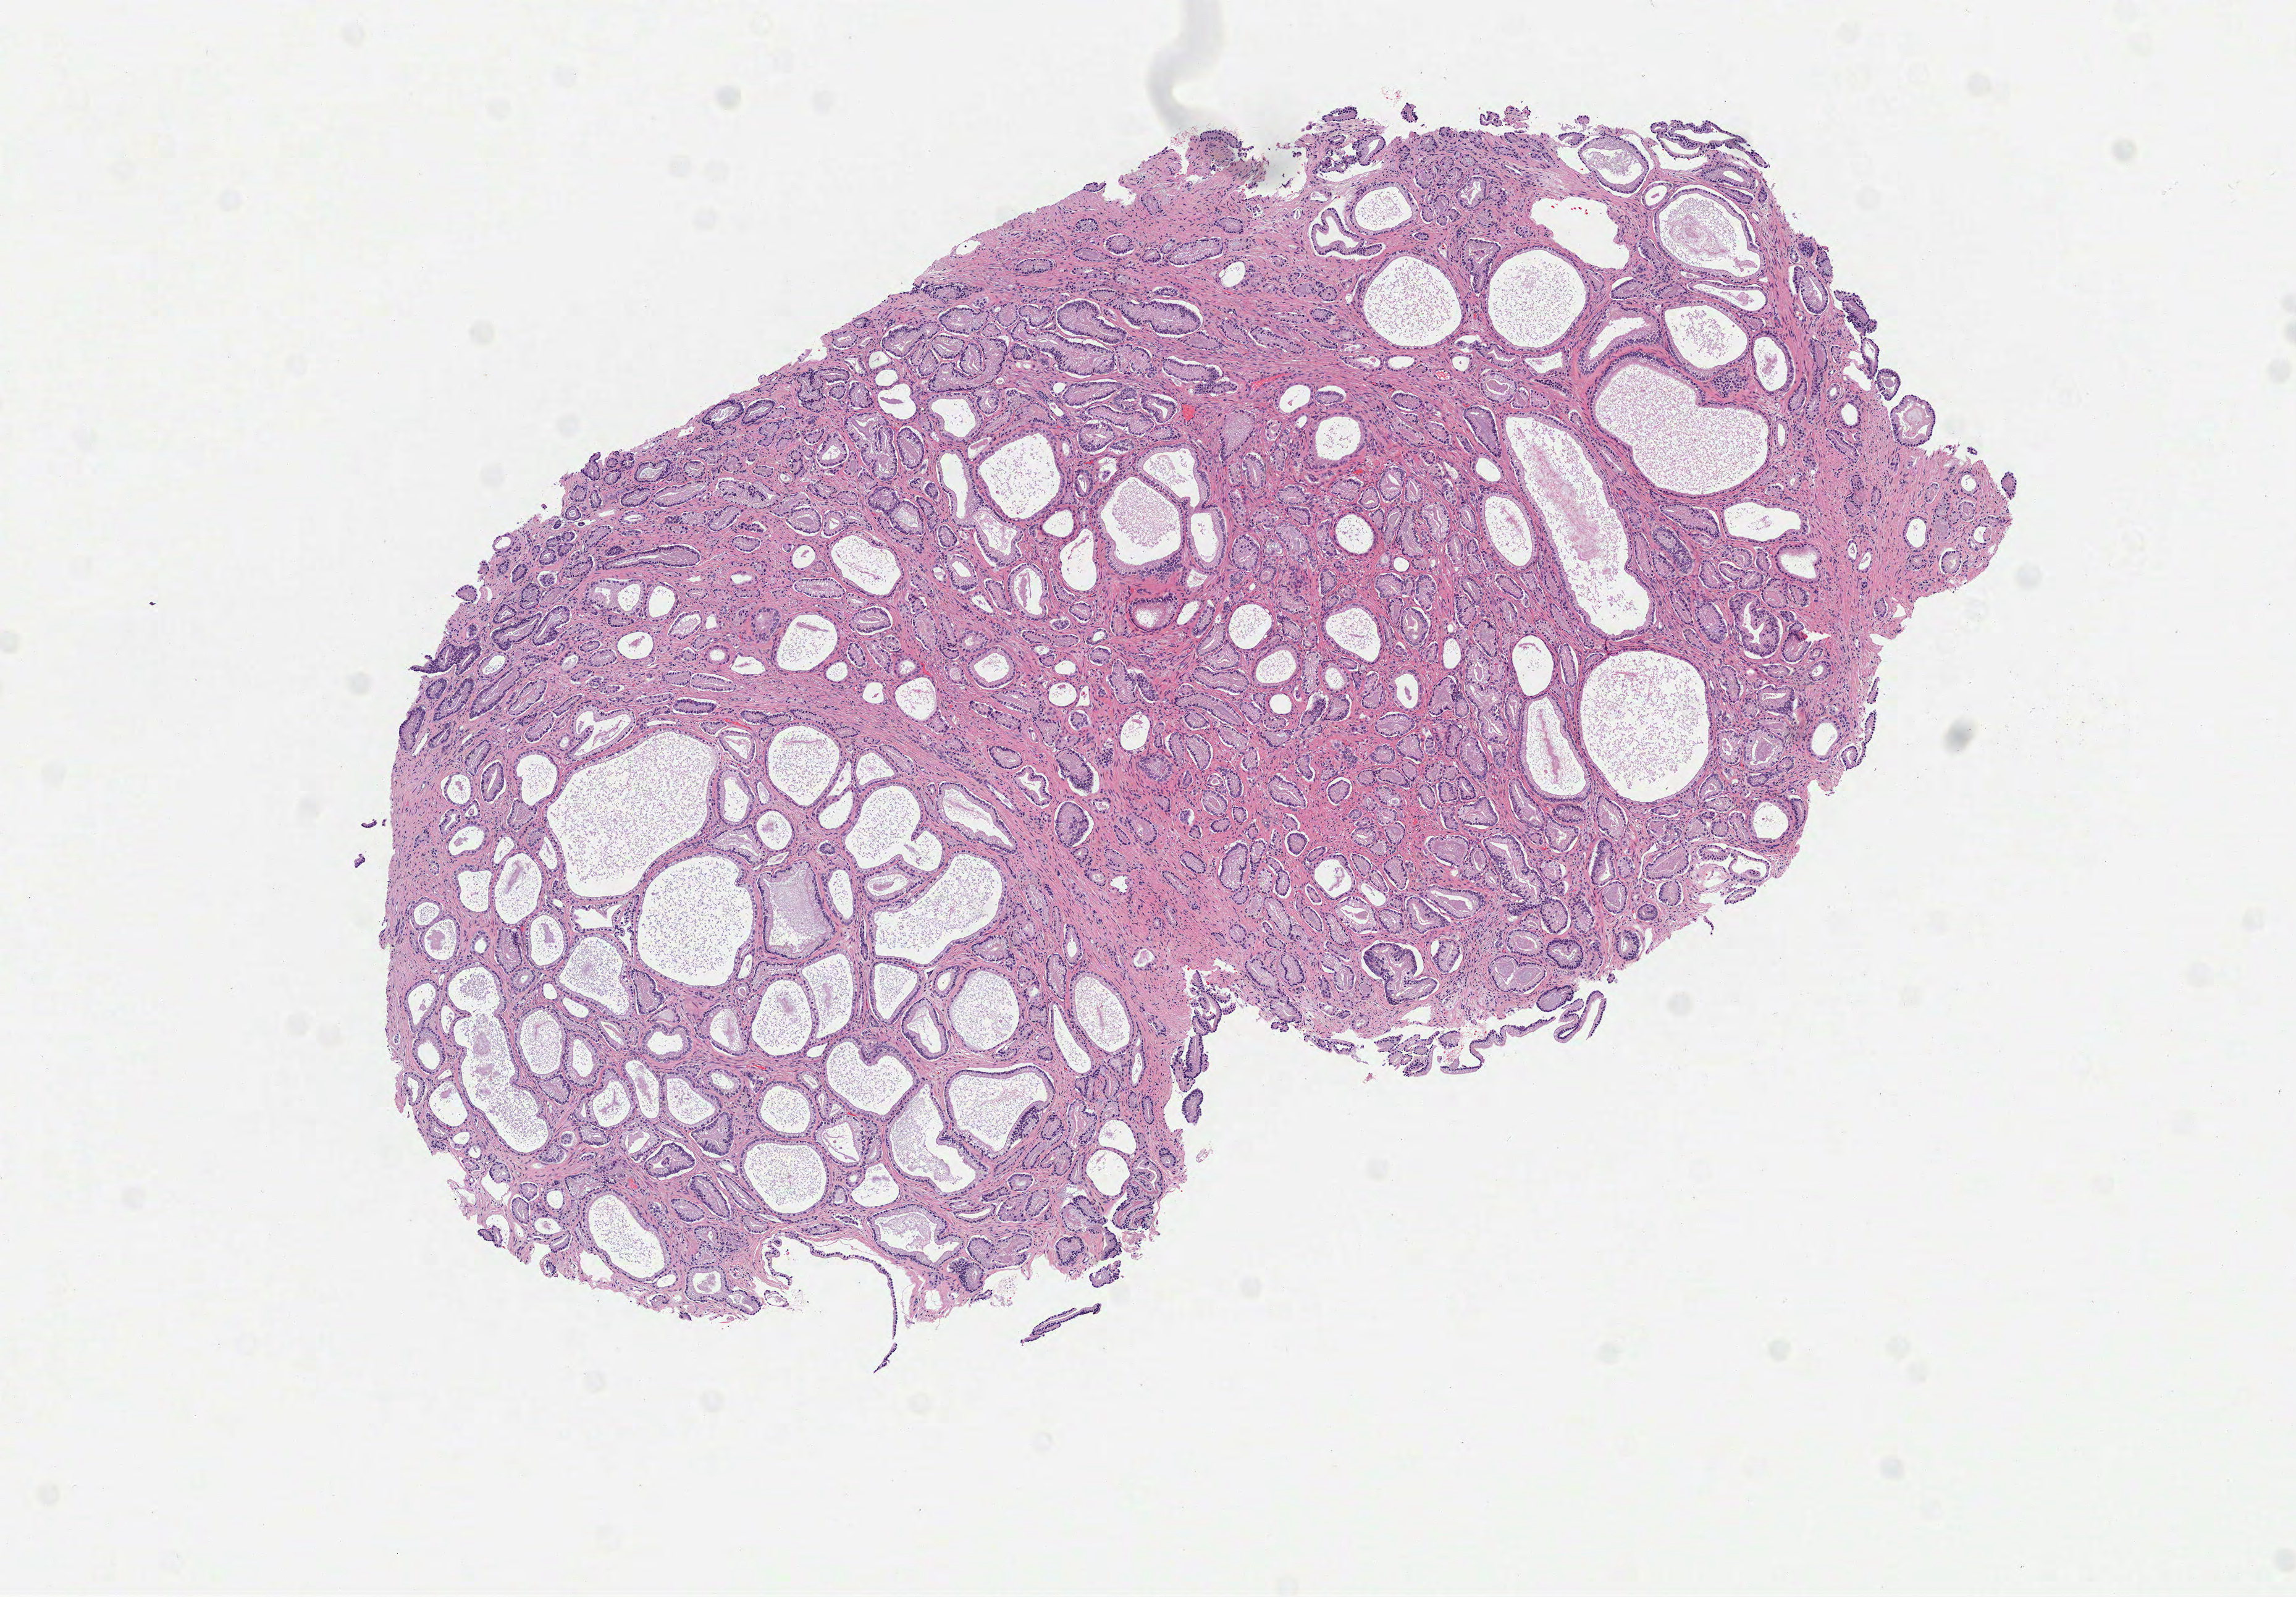
Whole-slide histology image, Hematoxylin and eosin (H&E) stained, a low-resolution overview of the entire scanned area, about 7.5 x 5.2 mm (acquisition: 40x scan). Frozen section from the top of the tissue portion. Primary tumour sample from the prostate. Male, age 68 years at initial diagnosis. Gleason score: 7 (3+4). Composition of this section per pathologist review: tumour cells 75%, tumour nuclei 75%, normal cells 10%, stromal cells 15%, necrosis 0%.
Pathologic diagnosis: Acinar cell carcinoma (prostate gland).